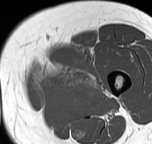
MRI of an extremity soft-tissue mass, one axial slice. Position 15 of 57 along the scan axis. MR volume resampled by the dataset authors to the PET/CT grid (not the native acquisition matrix). 152 × 144 image matrix, field of view 148 × 141 mm. Female patient. From the clinical record (not read from this slice): histological type: pleiomorphic leiomyosarcoma; grade: intermediate; site of the primary tumour: left thigh.
Outlined on this slice (expert contour drawn on MRI and transferred to this co-registered scan by the dataset authors):
- gross tumour volume including surrounding oedema: bounding box [x1, y1, x2, y2] px = [36, 58, 101, 97]